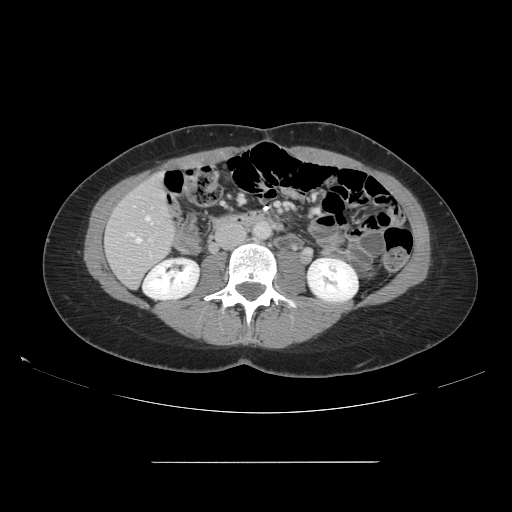
Contrast-enhanced abdominal CT, one axial slice. 120 kVp. Soft-tissue window (W 400 / L 40 HU). 2.5 mm slice thickness. 512 × 512 image matrix, field of view 421 × 421 mm. Female patient, age 46 years. Case-level facts recorded for this patient, not image findings: diagnosis: colorectal cancer liver metastases, imaged before liver resection; multiple liver metastases: yes; largest metastasis: 3 cm; disease in both lobes: yes.
Outlined on this slice (expert manual segmentation):
- hepatic veins: bounding box [x1, y1, x2, y2] px = [136, 216, 151, 242]
- liver: [106, 175, 176, 287]
- planned liver remnant (the part of the liver to remain after resection): [106, 176, 175, 287]